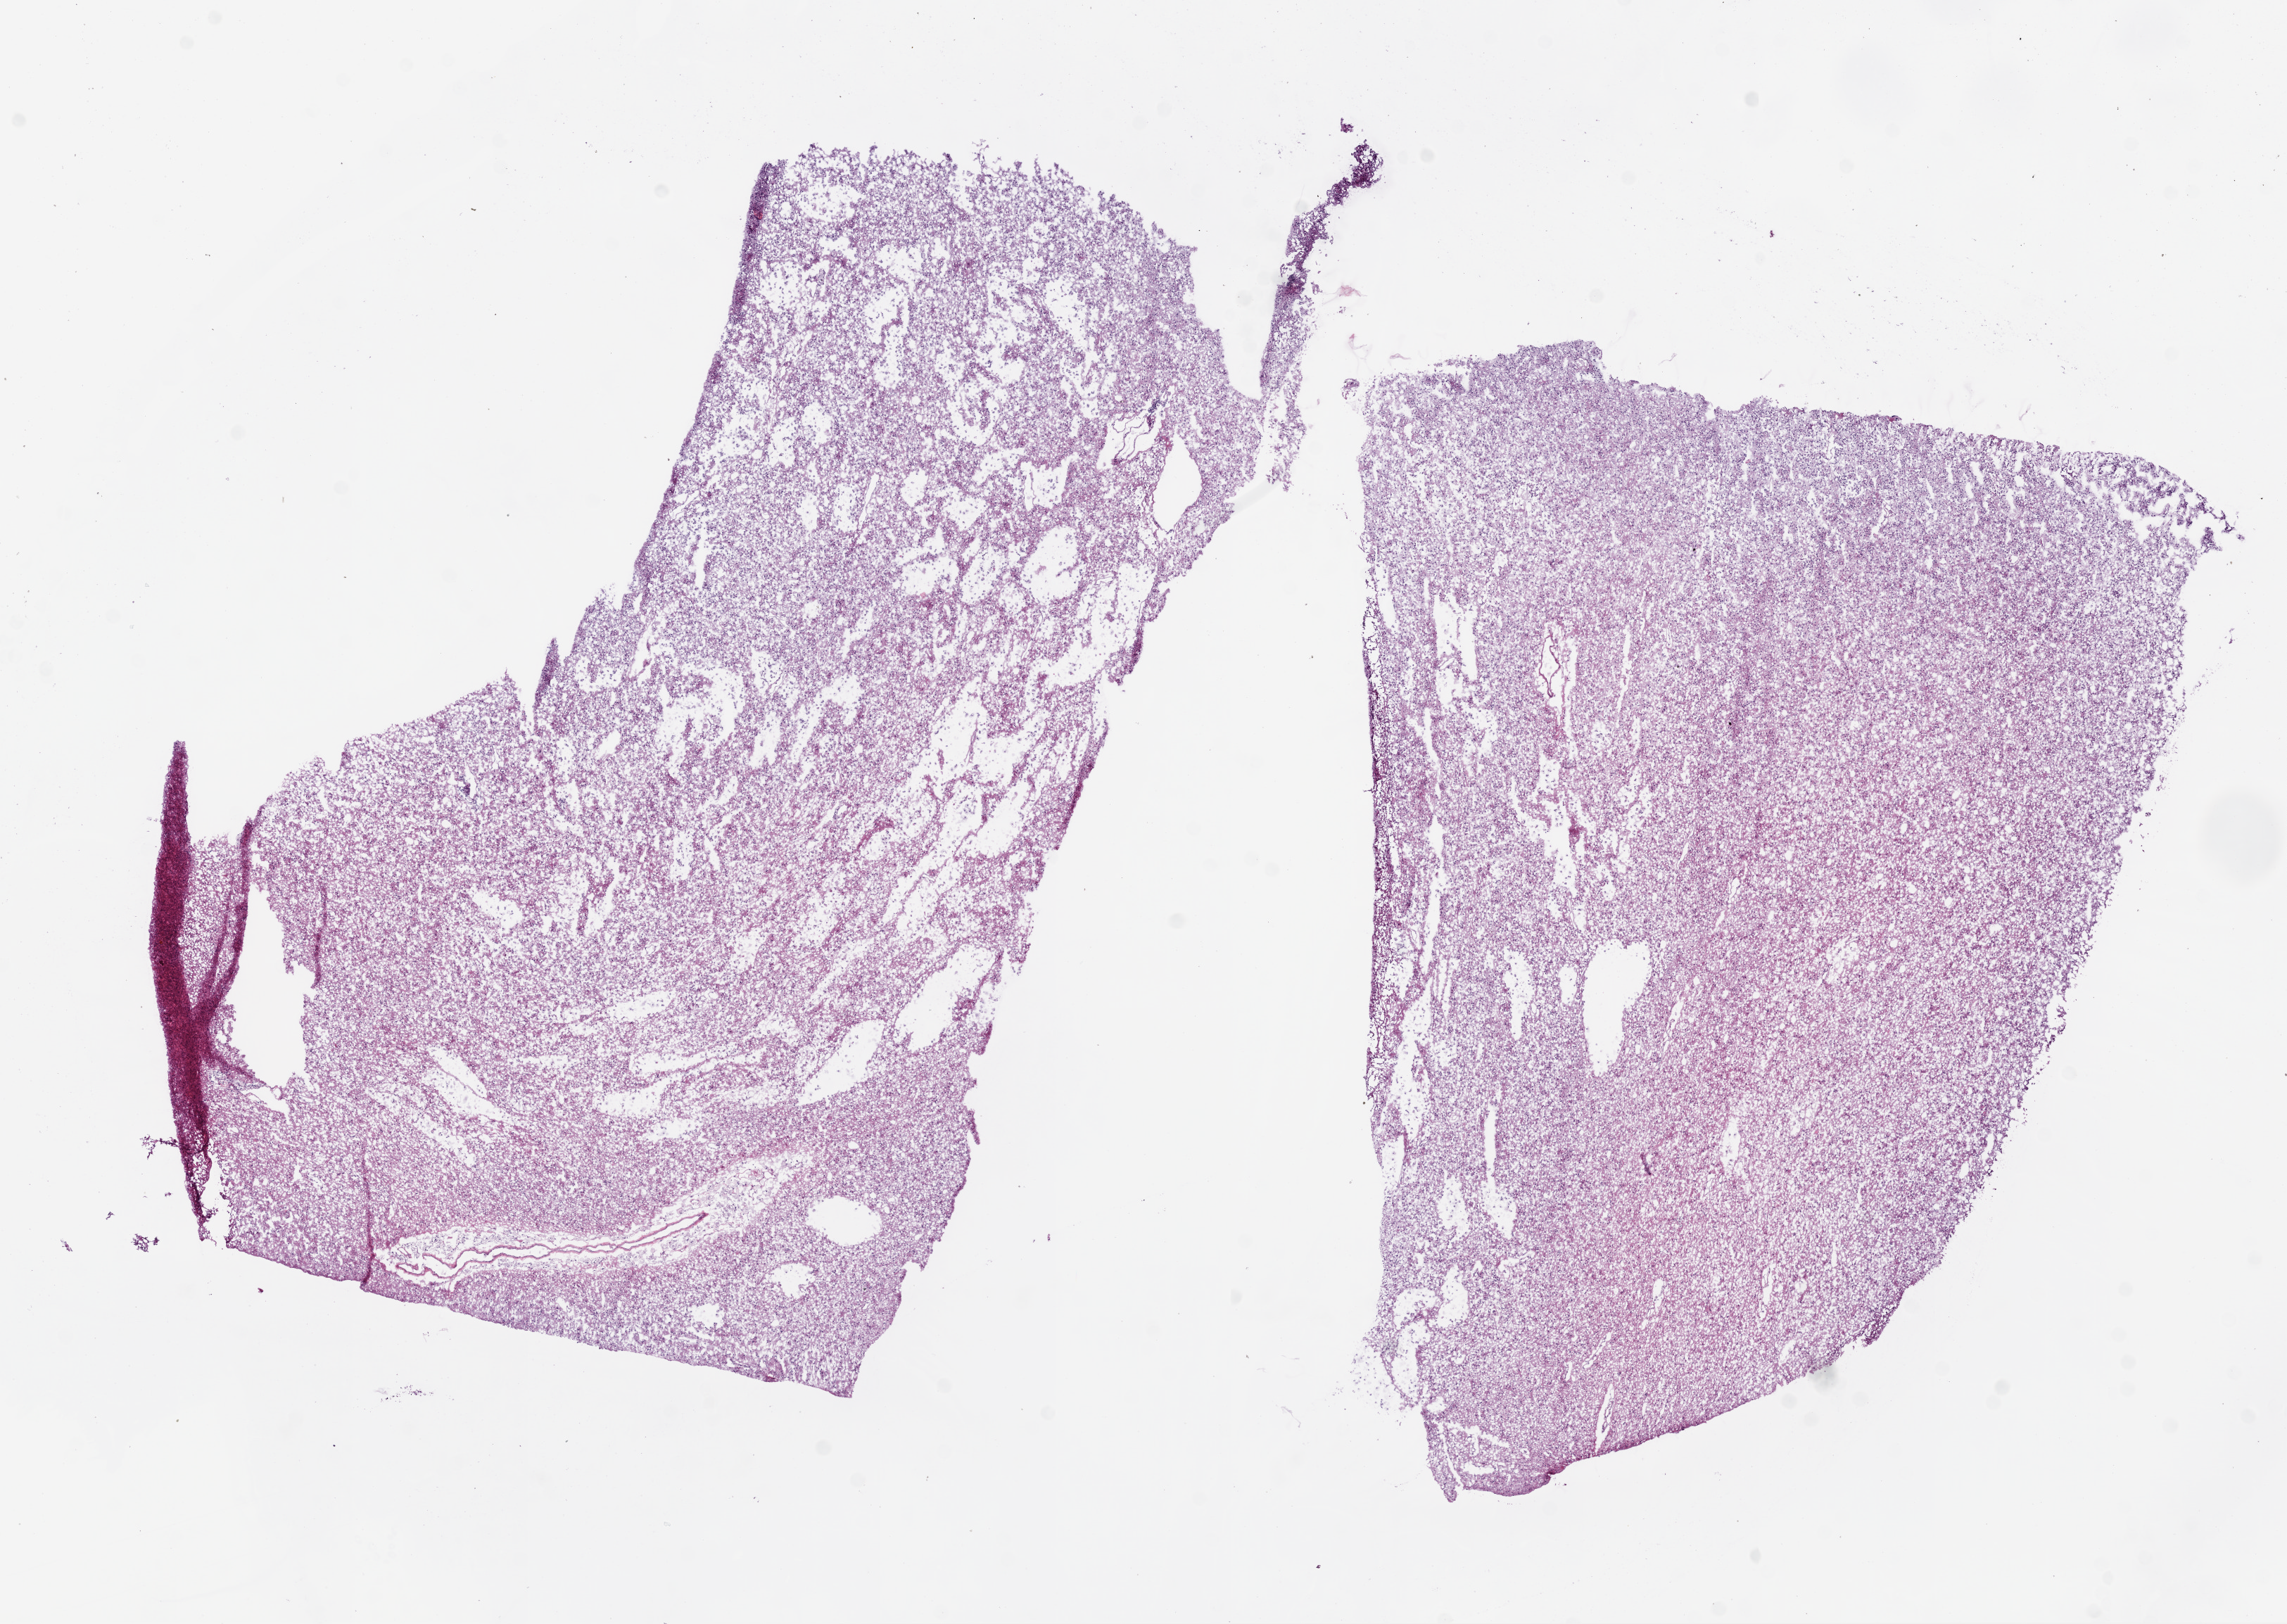
Digitized H&E tissue section (whole slide), whole scanned area (about 13.0 x 9.3 mm) shown as a low-resolution overview, frozen section, sample: primary tumour, brain. Female patient; age at initial diagnosis 48 years.
Histologic diagnosis: Oligodendroglioma, NOS.